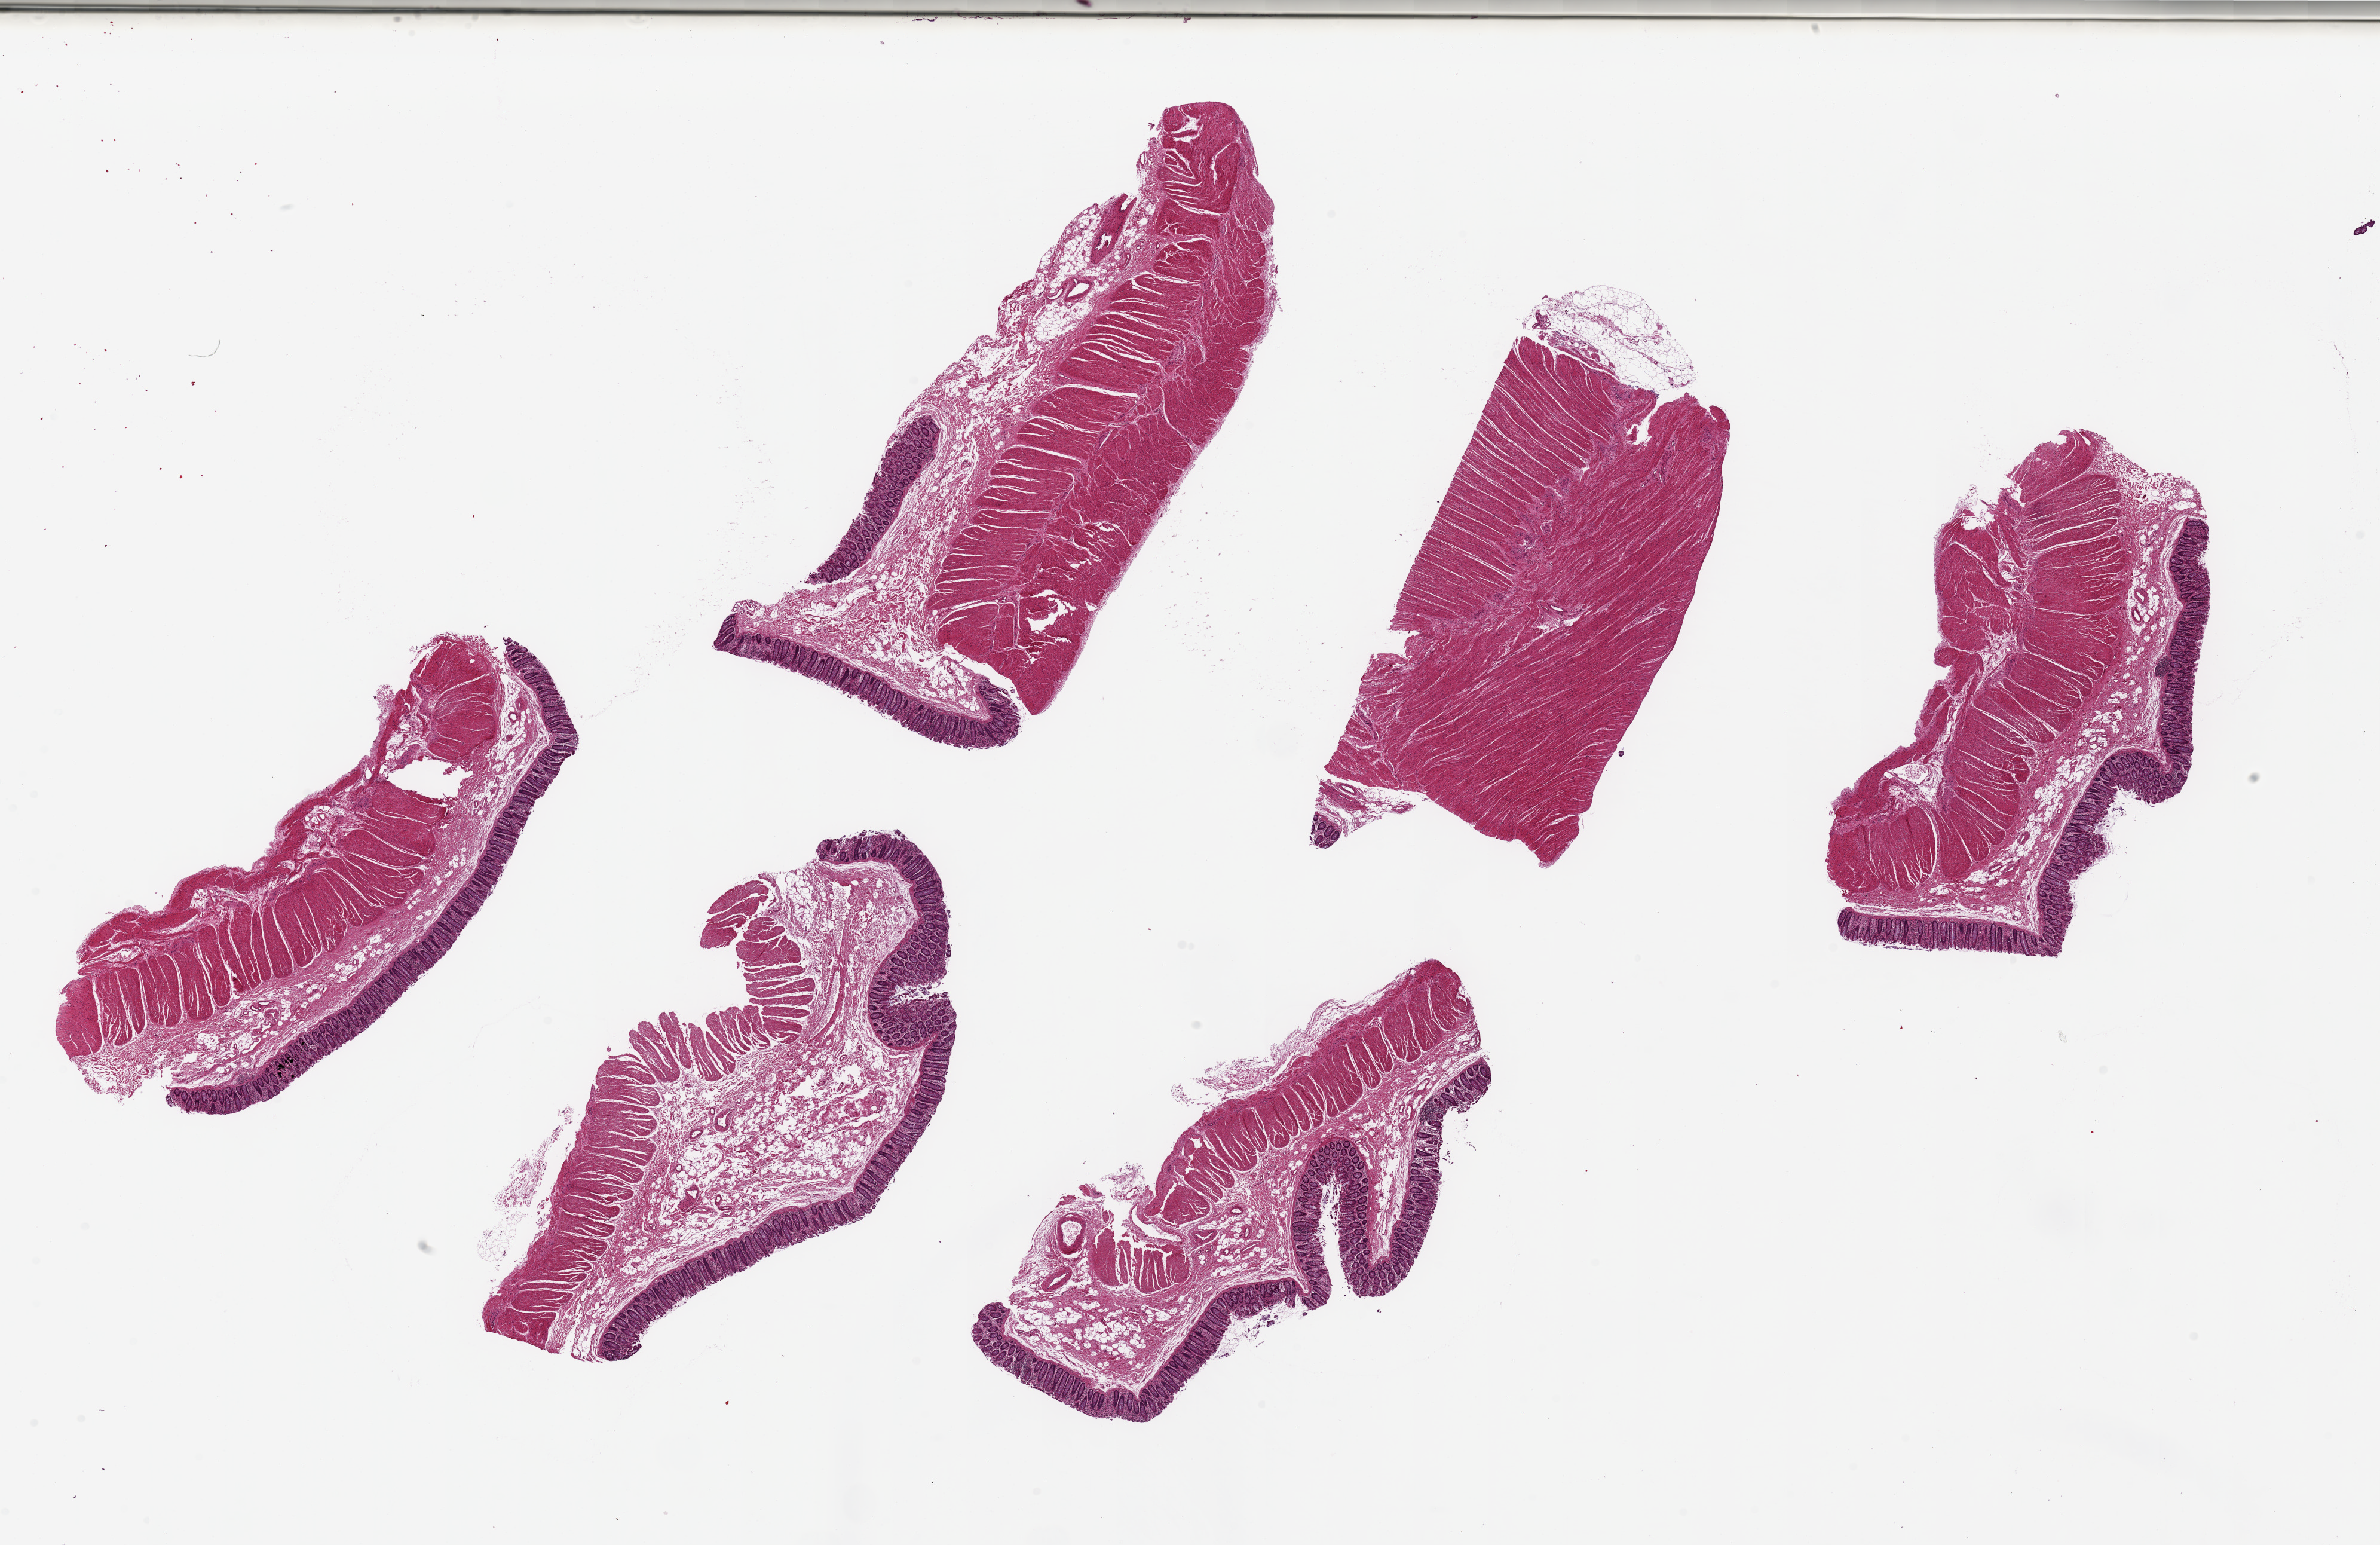
Haematoxylin and eosin whole-slide image, shown as a low-resolution overview of the whole scanned area (about 31.5 x 20.4 mm, slide scanned at 20x), PAXgene-fixed paraffin-embedded (PFPE) section, section of sigmoid colon (target tissue), donor tissue sample. Male donor.
- pathologist's review note for this sample: 6 pieces, up to 9x4mm; ~60% muscularis; rest is fat and mucosa